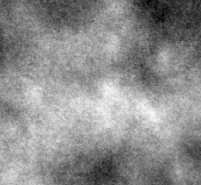
Region of interest cut from a scanned film mammogram (one marked finding); left breast; CC view; BI-RADS breast density category 2 (scale 1–4).
Marked abnormality: calcifications, morphology lucent center; BI-RADS assessment category 2; benign; no additional work-up was recommended (benign without callback).